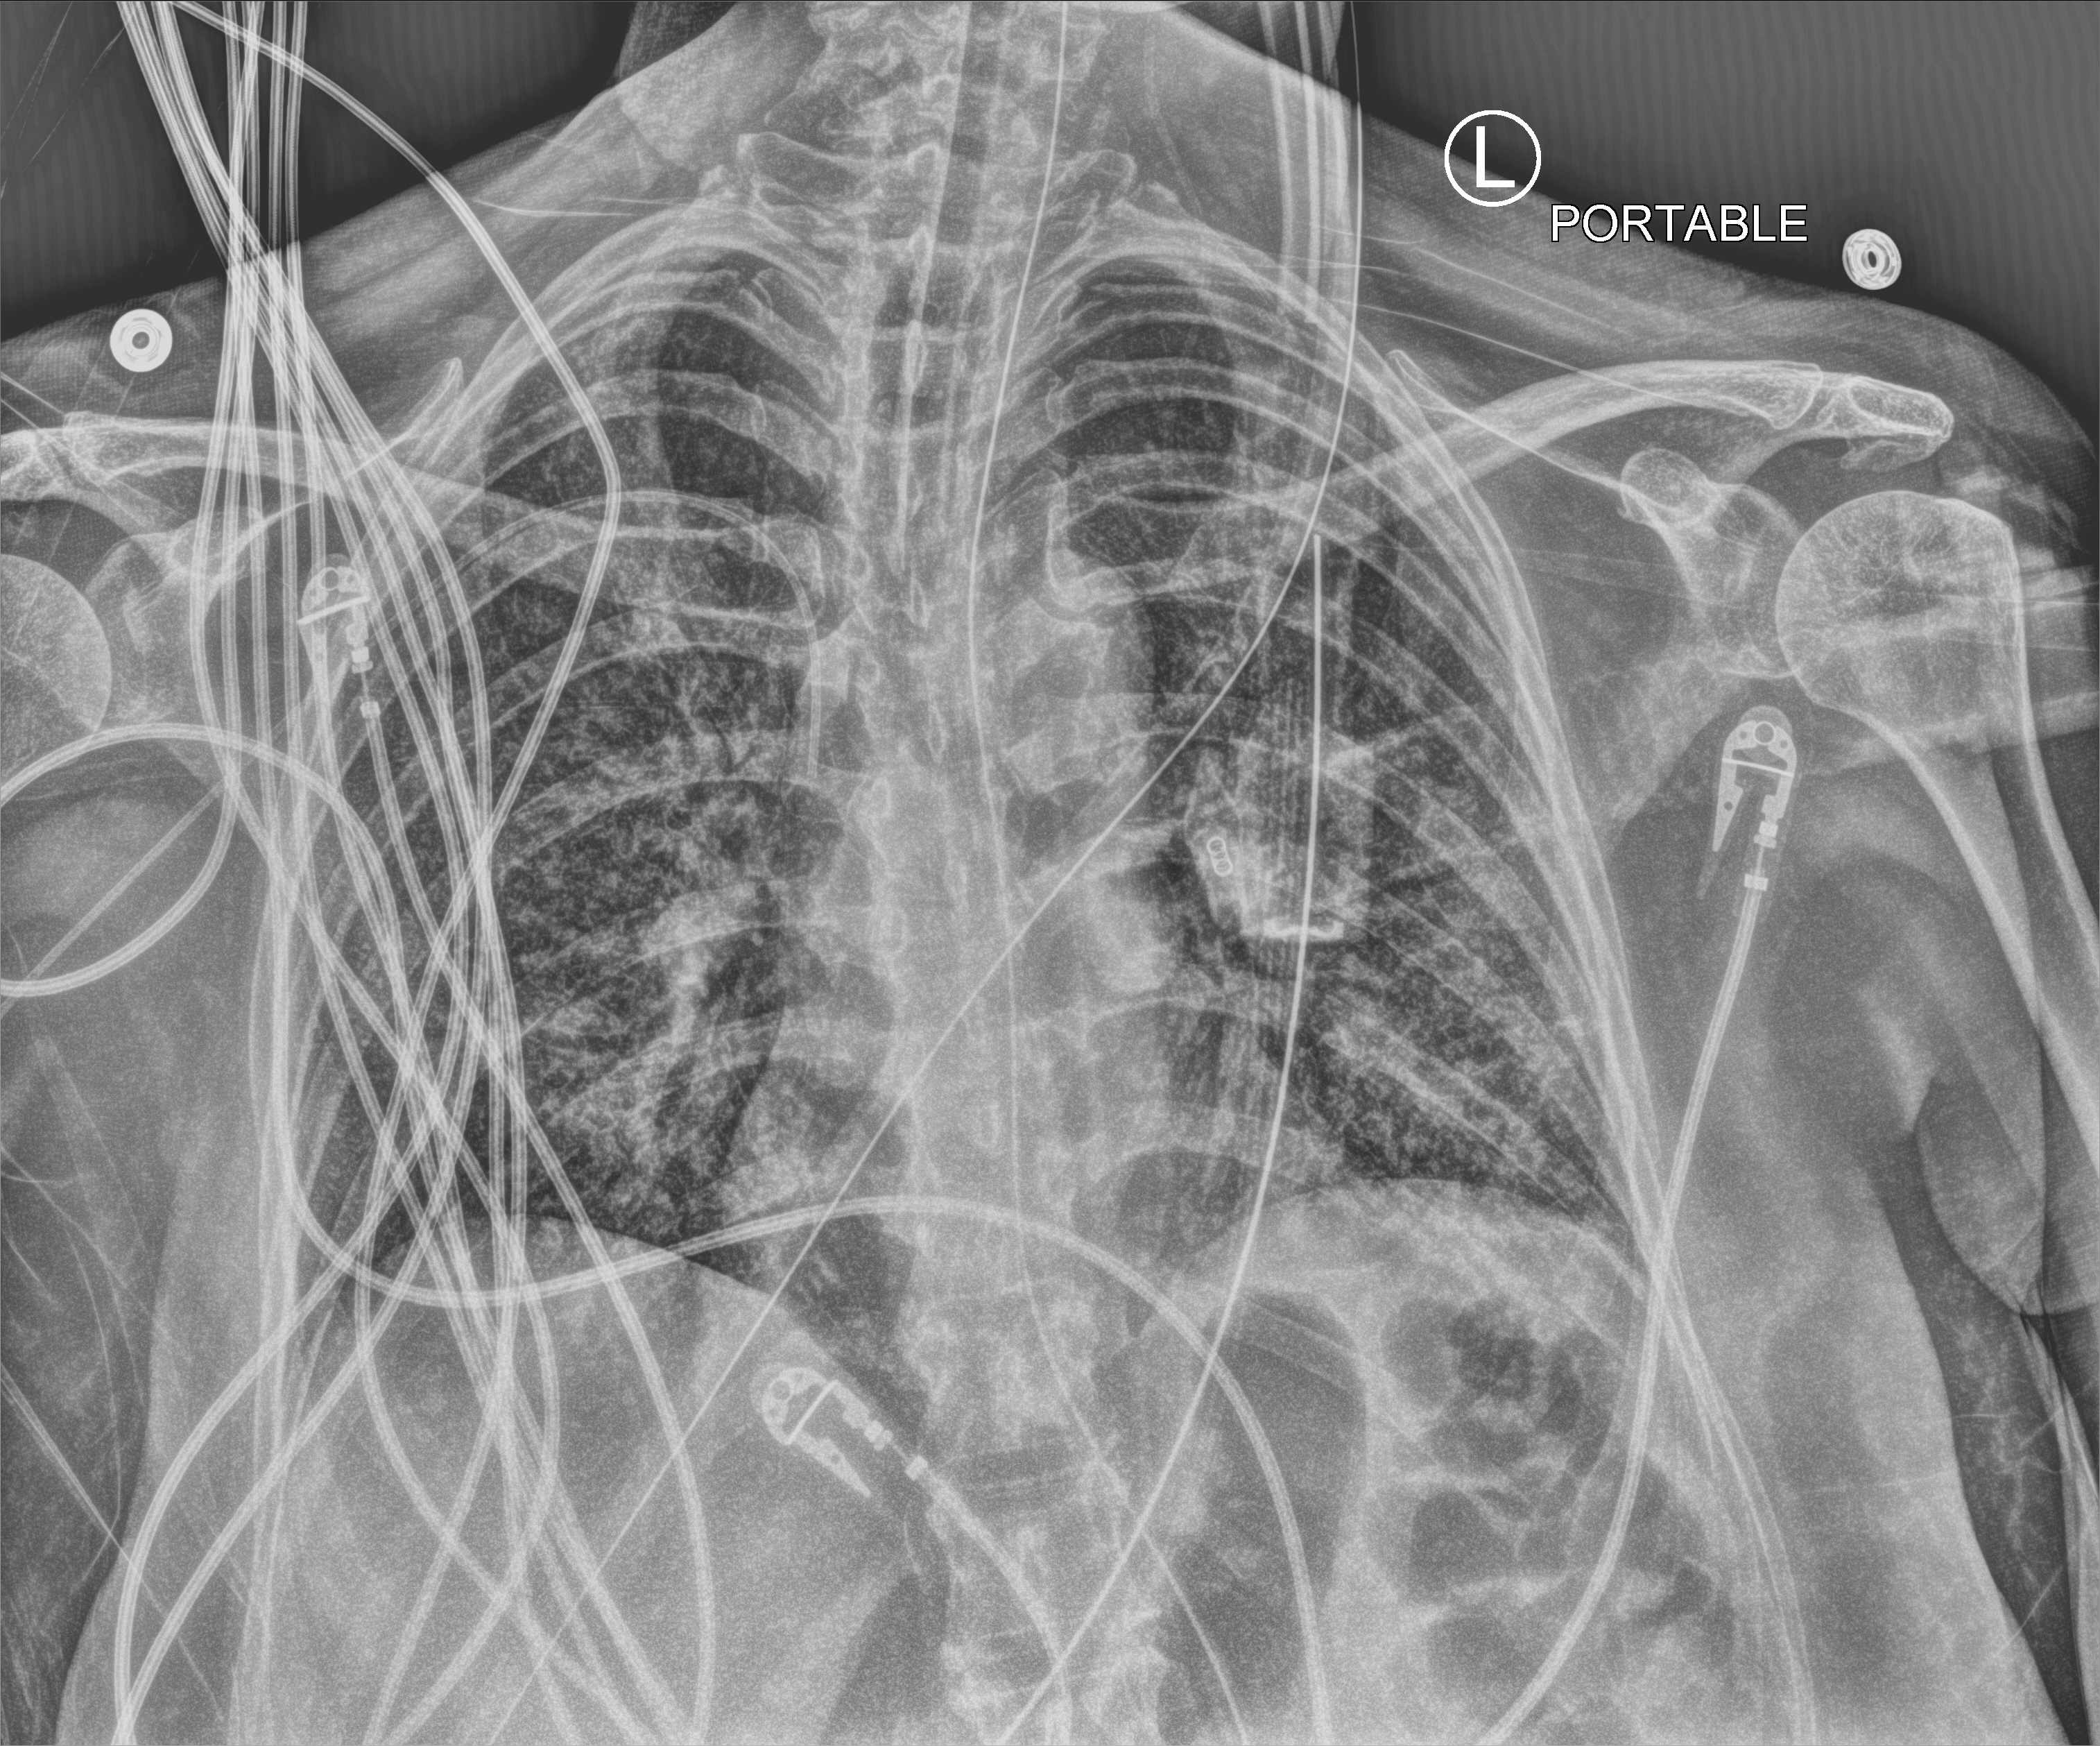
Chest X-ray (portable), anteroposterior (AP) projection. Patient hospitalised with COVID-19; female, aged 60–74 years.
Hospital-stay facts (about this admission, not read from this image; timing relative to this image not recorded): COPD (admission record): no.